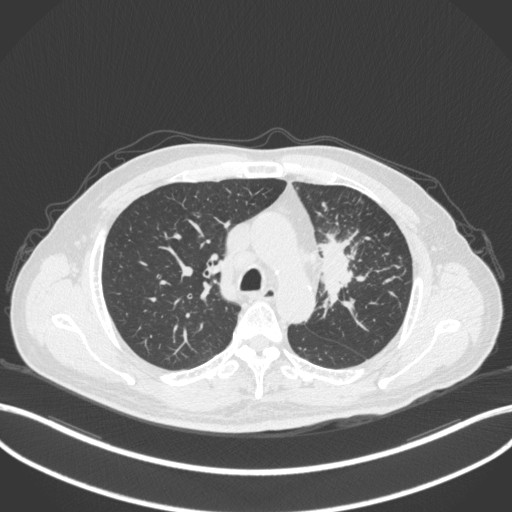
Chest CT, one axial slice; slice 243 of 386 in the series (ordered by position); reconstruction kernel B31f; 120 kVp; lung window (W 1500 / L -600 HU); 512 × 512 image matrix, field of view 400 × 400 mm. Patient: male, 69 years. From the clinical record (not read from this slice): clinical TNM (as recorded): T2a N2 M0; histopathological grade: G2-3.
Outlined on this slice (bounding box drawn by a radiologist):
- lung tumour (recorded histology: adenocarcinoma): bounding box <313,230,369,319> (left, top, right, bottom; pixels)